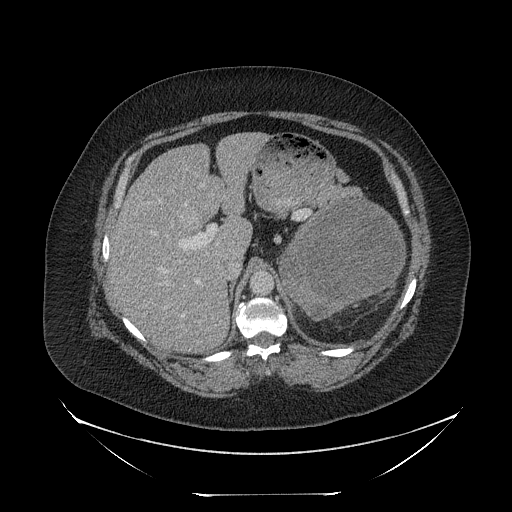
Contrast-enhanced abdominal CT, one axial slice; position 157 of 205 along the scan axis; reconstruction kernel STANDARD; soft-tissue window (W 400 / L 40 HU); 512 × 512 image matrix. Female patient, age 53 years. Case-level facts recorded for this patient, not image findings: diagnosis: adrenocortical carcinoma; tumour side: left adrenal; tumour size at pathology: 17 cm; Ki-67 index: 20 %; stage (as recorded): 3.
Structures marked on this image (semi-automatic segmentation, software-assisted and operator-edited):
- mass: bounding box (x1, y1, x2, y2) in pixels: (281, 200, 403, 316)